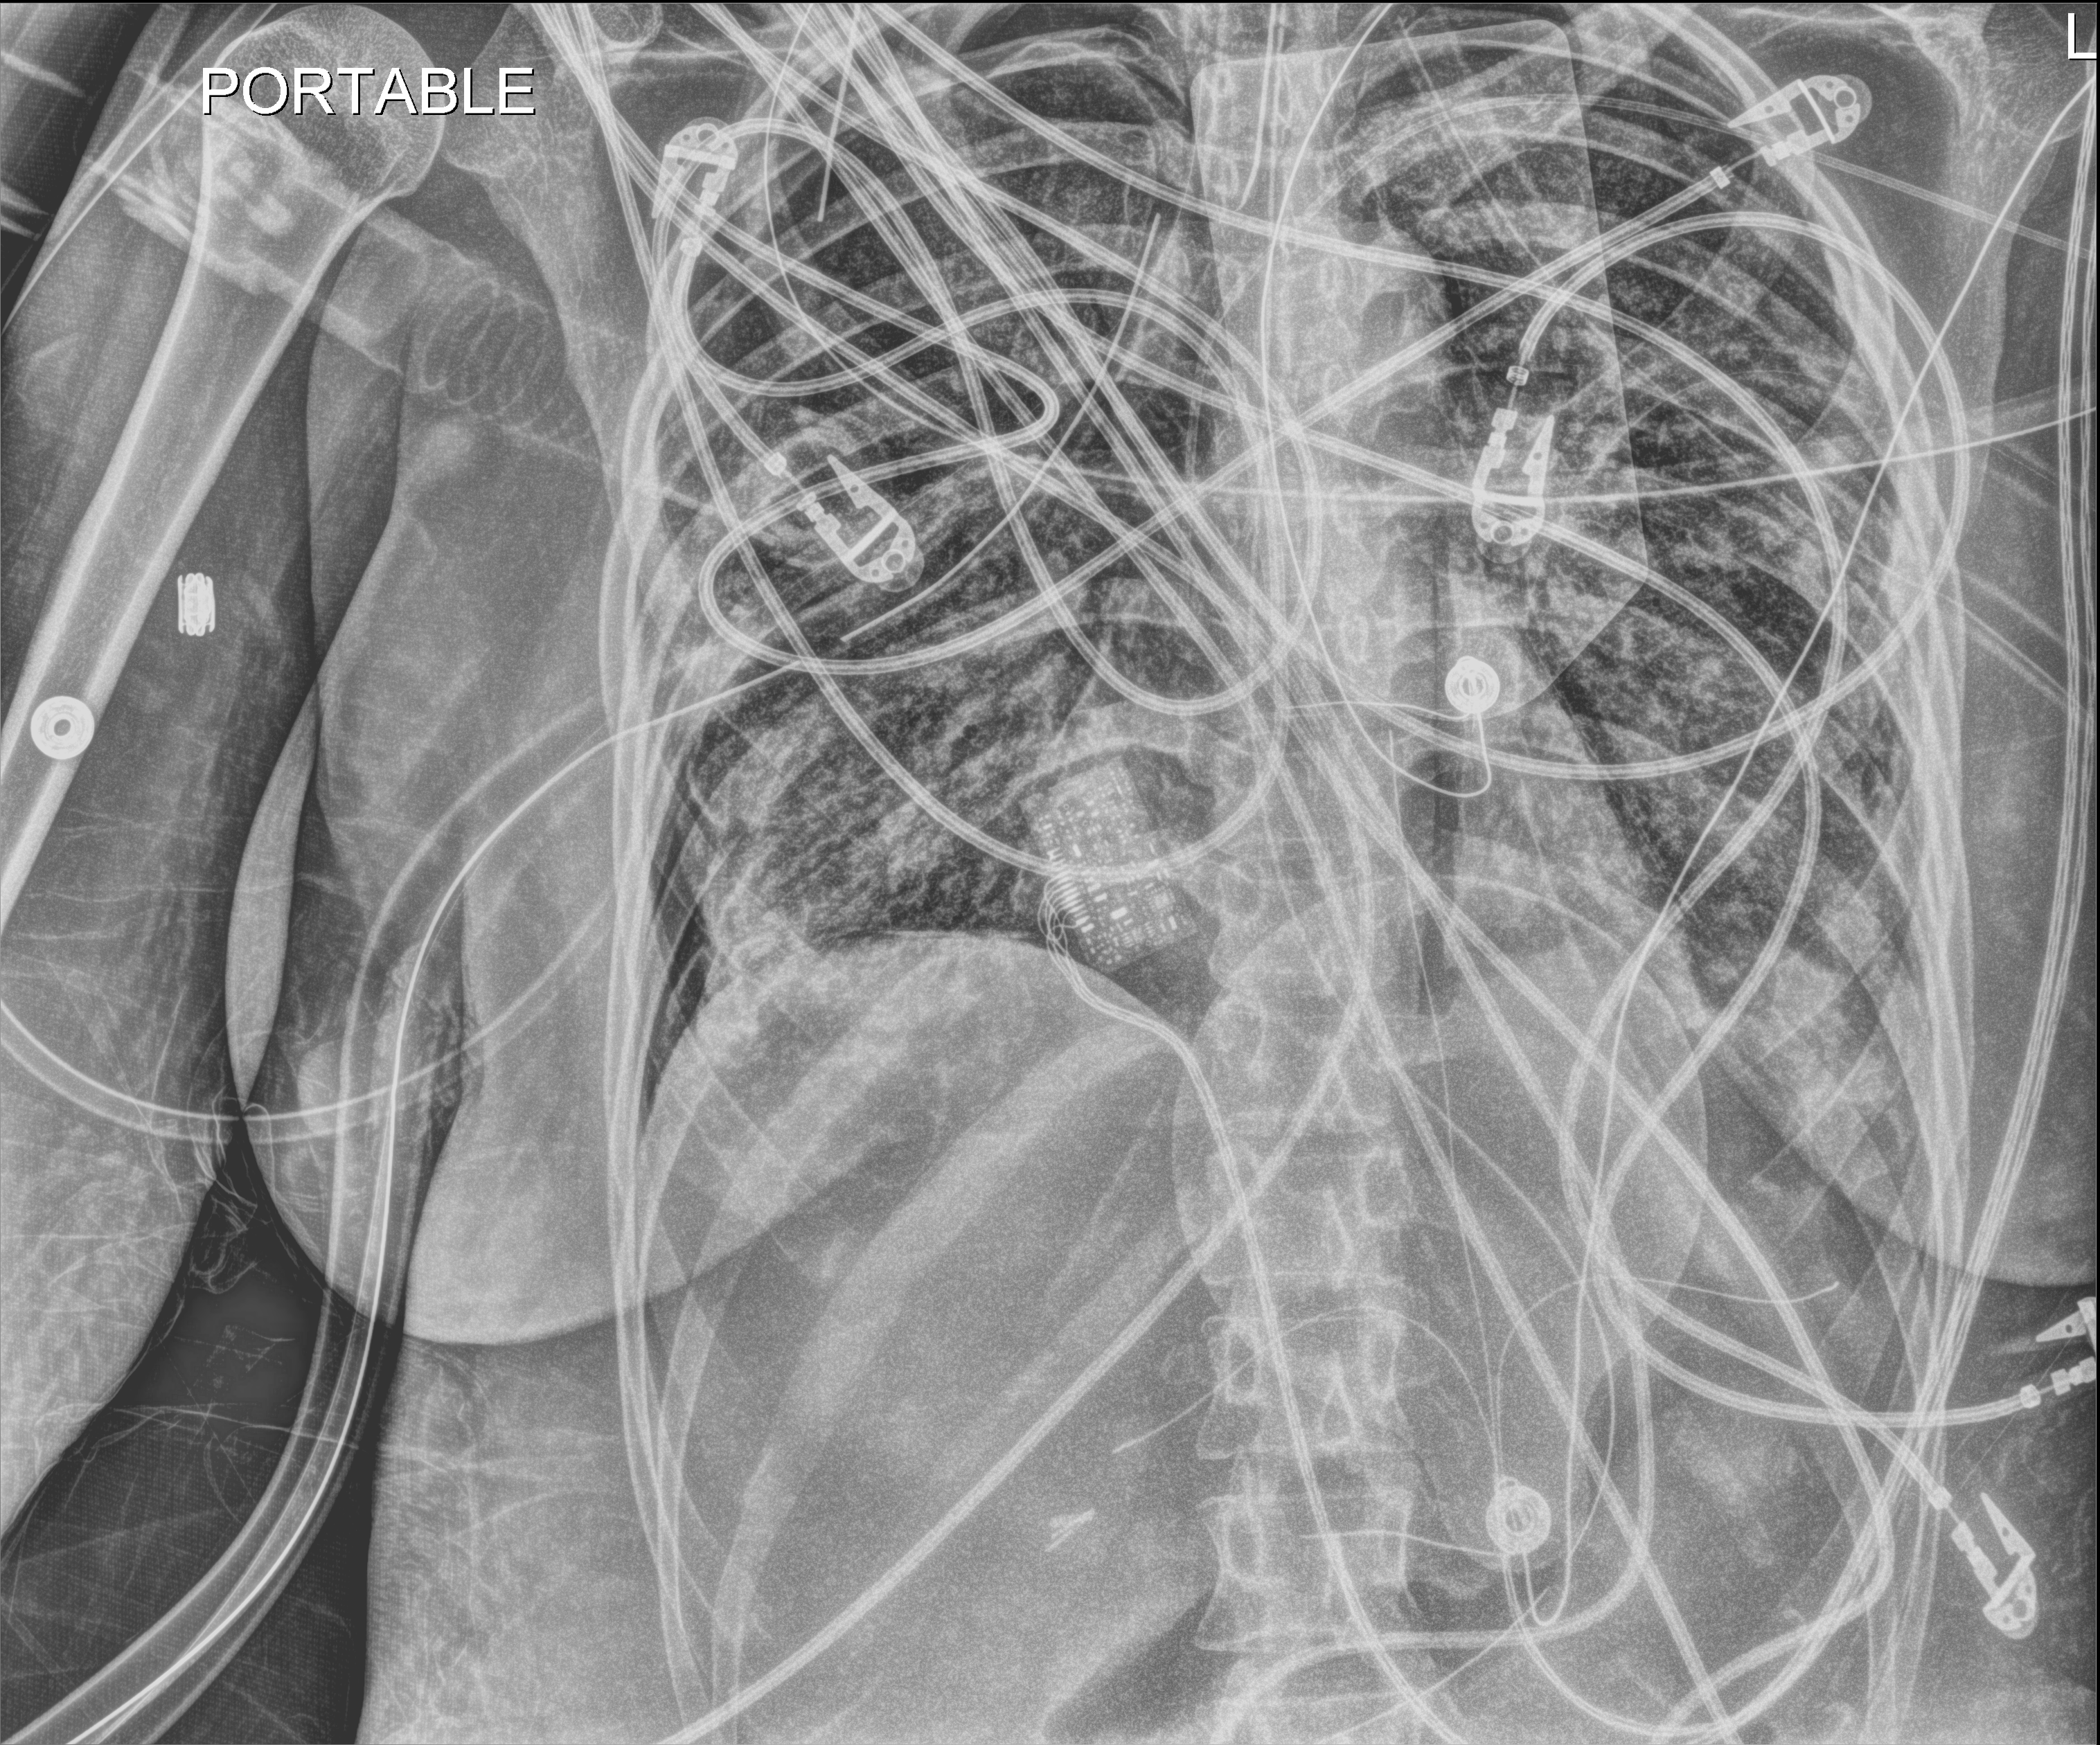
Bedside chest radiograph (digital radiography); anteroposterior (AP) projection. Adult patient hospitalised with COVID-19, age 18–59 years.
From the hospital-stay record, not from the radiograph (when in the stay this image was taken is not recorded): hypertension (admission record): no.